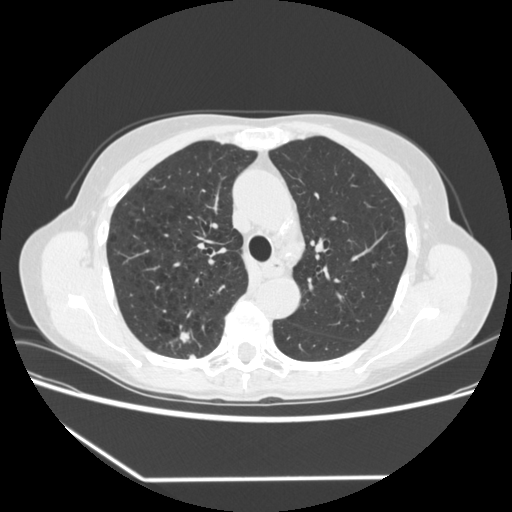
Low-dose screening chest CT, one axial slice. Slice 234 of 323 in the series (ordered by position). Lung window (W 1500 / L -600 HU). 512 × 512 image matrix, field of view 360 × 360 mm.
Annotated regions visible in this slice (manually delineated by an expert):
- lesion 1 (tumor, upper lobe of right lung): bounding box (x1, y1, x2, y2) in pixels: (180, 332, 193, 343)